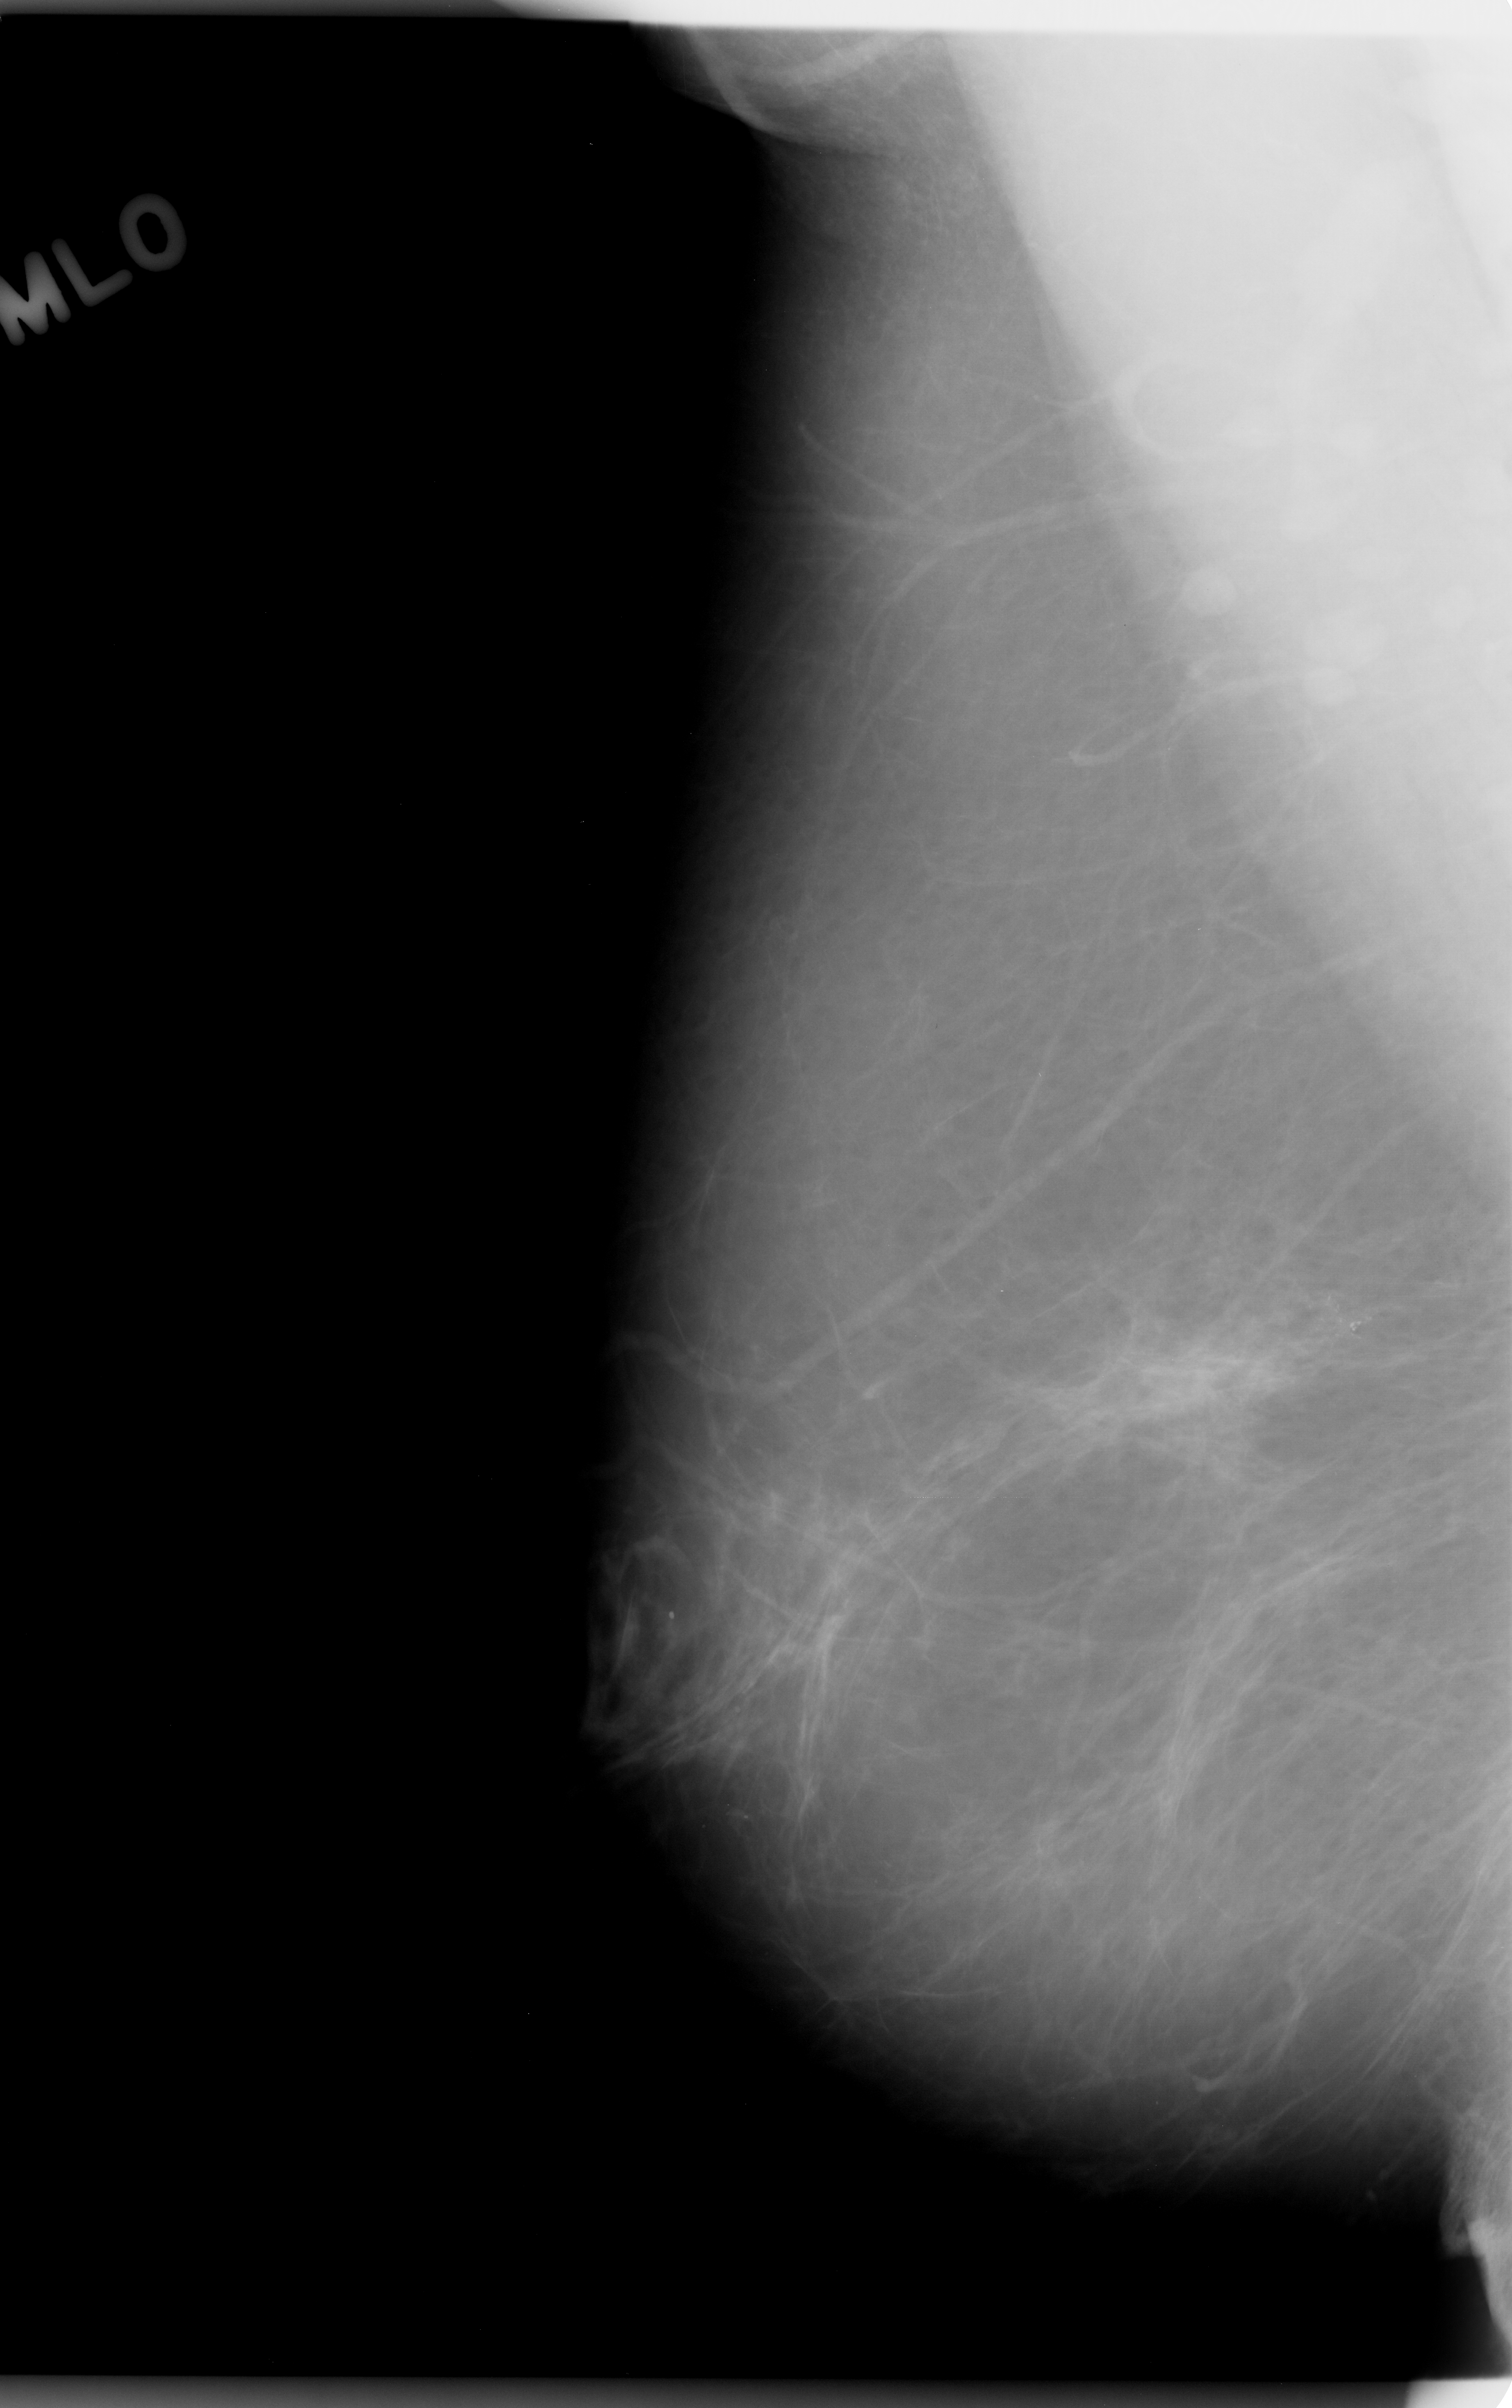
Scanned film-screen mammogram; right breast; MLO view; breast composition: almost entirely fatty (BI-RADS density category 1 of 4); 1512 × 2408 image matrix.
Expert-marked regions of interest on this image (one box per marked abnormality):
- calcifications, morphology amorphous, distribution clustered; BI-RADS assessment category 4; subtlety rating 4 on a 1 (subtle) to 5 (obvious) scale; pathology result (as recorded, not read from the image): malignant: bounding box [x1, y1, x2, y2] px = [1275, 1259, 1437, 1425]